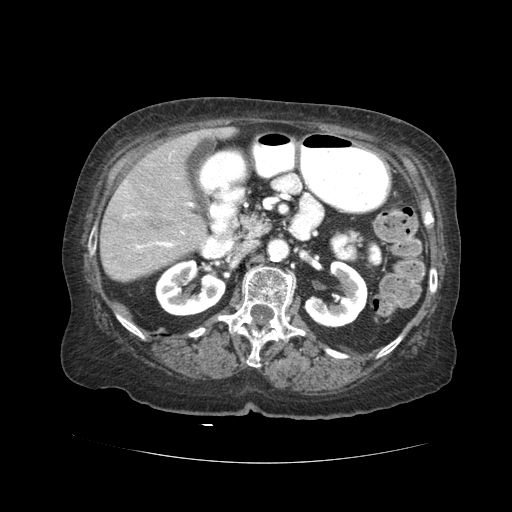
Contrast-enhanced abdominal CT (liver protocol), one axial slice. Position 11 of 59 along the scan axis. 120 kVp. Soft-tissue window (W 400 / L 40 HU). 2.5 mm slice thickness. 512 × 512 image matrix, field of view 380 × 380 mm. Case-level facts recorded for this patient, not image findings: diagnosis: hepatocellular carcinoma (patient treated with transarterial chemoembolisation; whether this scan precedes or follows treatment is not stated here); TNM stage (as recorded): Stage-I; Child-Pugh class: A.
Outlined on this slice (semi-automatic segmentation, software-assisted and operator-edited):
- liver parenchyma outside the tumour (the mass and vessels are separate outlines, so this box may not span the whole liver): box from (x=100, y=126) to (x=235, y=282) px
- liver vessels: (x=123, y=202)–(x=193, y=249)